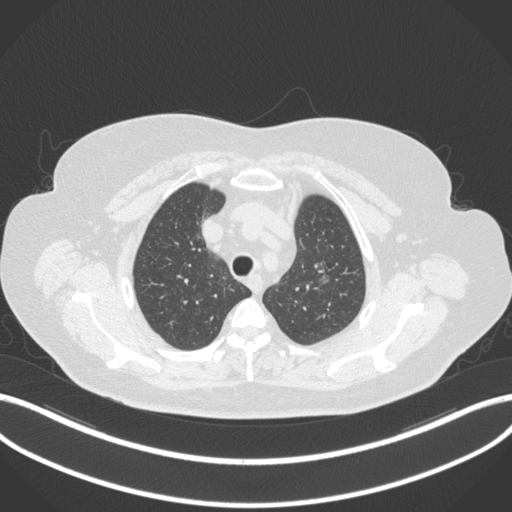
Chest CT, one axial slice. Position 273 of 310 along the scan axis. Lung window (W 1500 / L -600 HU). 512 × 512 image matrix, field of view 400 × 400 mm. Patient: female, 70 years. Case-level facts recorded for this patient, not image findings: clinical TNM (as recorded): T1c N0 M0.
Outlined on this slice (bounding box drawn by a radiologist):
- lung tumour (recorded histology: adenocarcinoma): bounding box <311,257,334,288> (left, top, right, bottom; pixels)